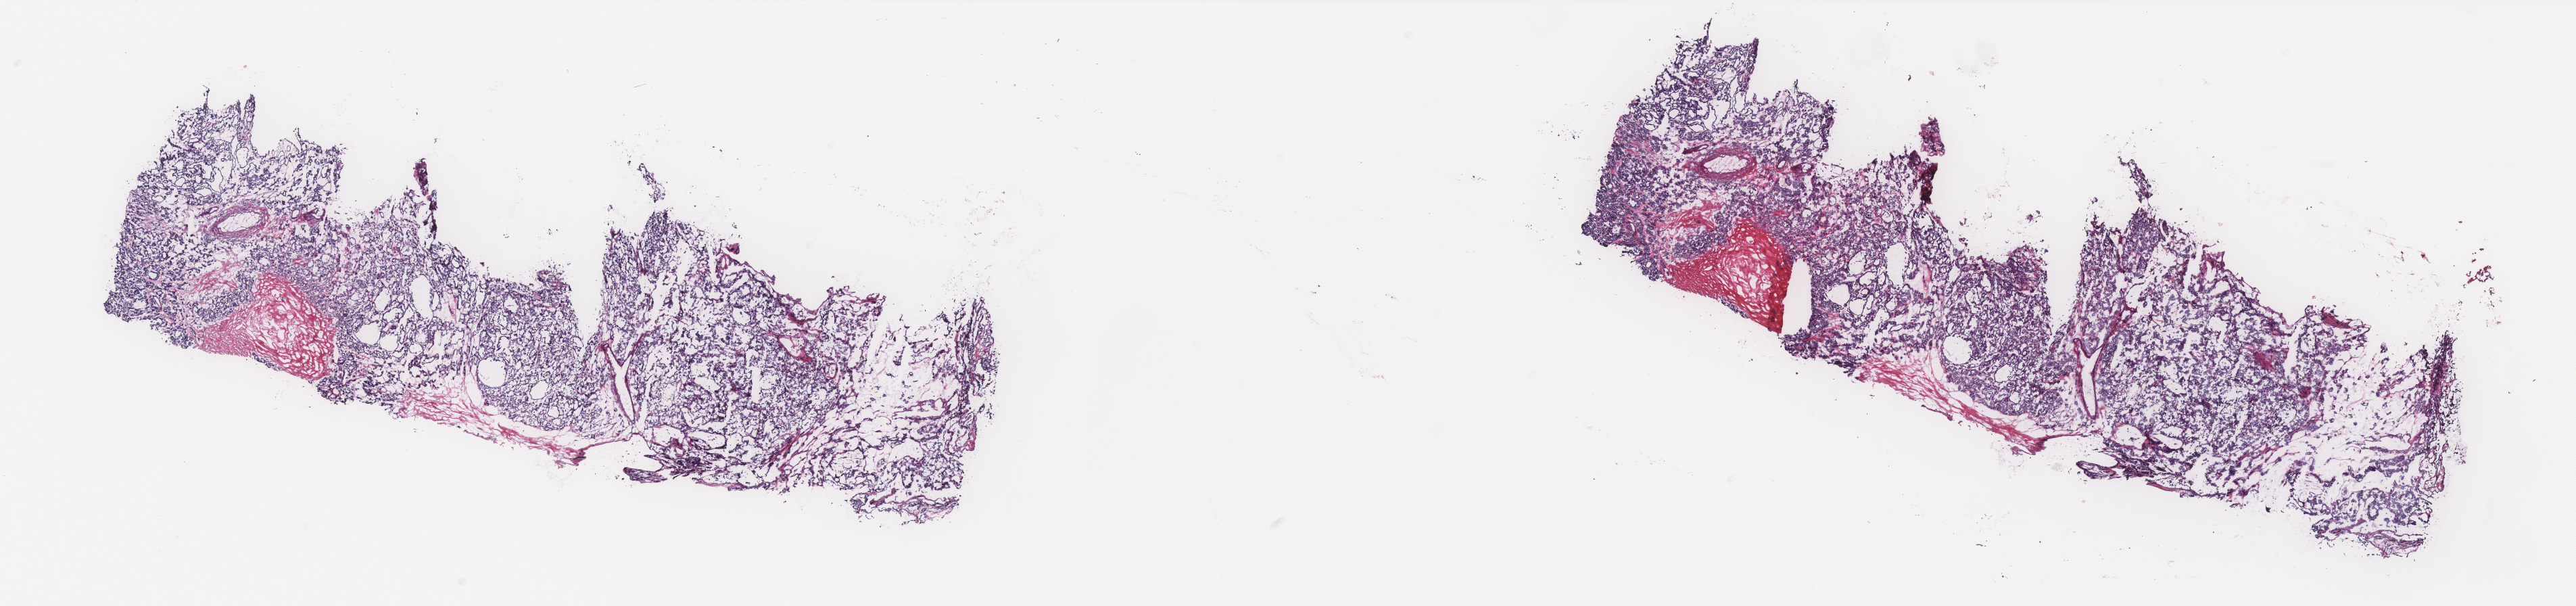
Whole-slide histology image, H&E-stained, a low-resolution overview of the entire scanned area, about 30.5 x 7.2 mm; frozen section from the bottom of the tissue portion; sample: primary tumour, thyroid. Female patient; age at initial diagnosis 67 years. Pathologist review of this section (percent, as recorded): tumour cells 85%, tumour nuclei 85%, normal cells 0%, stromal cells 15%, necrosis 0%. Infiltration values recorded for this section: lymphocyte infiltration 1%, monocyte infiltration 1%, neutrophil infiltration 0%.
Pathologic diagnosis: Papillary adenocarcinoma, NOS (thyroid gland). Lymph nodes positive (case pathology): 0 of 2 examined. AJCC pathologic stage: II (7th edition). TNM: T2 N0 M0. Laterality: bilateral.